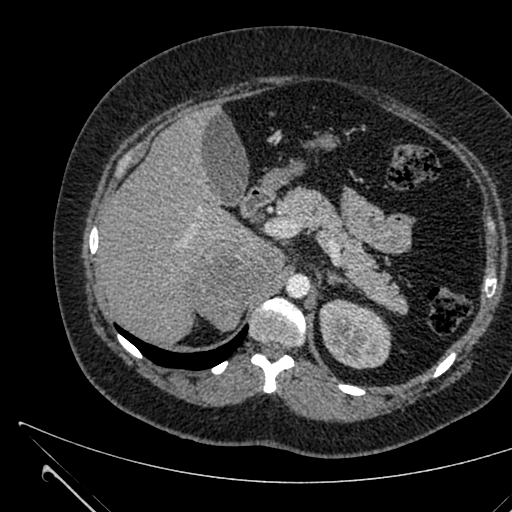
Contrast-enhanced abdominal CT, one axial slice; slice 434 of 731 in the series (ordered by position); 120 kVp; intravenous contrast given; soft-tissue window (W 400 / L 40 HU); 1 mm slice thickness; 512 × 512 image matrix. Patient: female, 36 years. Case-level facts recorded for this patient, not image findings: diagnosis: adrenocortical carcinoma; tumour side: right adrenal.
Outlined on this slice (semi-automatic segmentation, software-assisted and operator-edited):
- mass: bounding box [x1, y1, x2, y2] px = [194, 243, 284, 329]